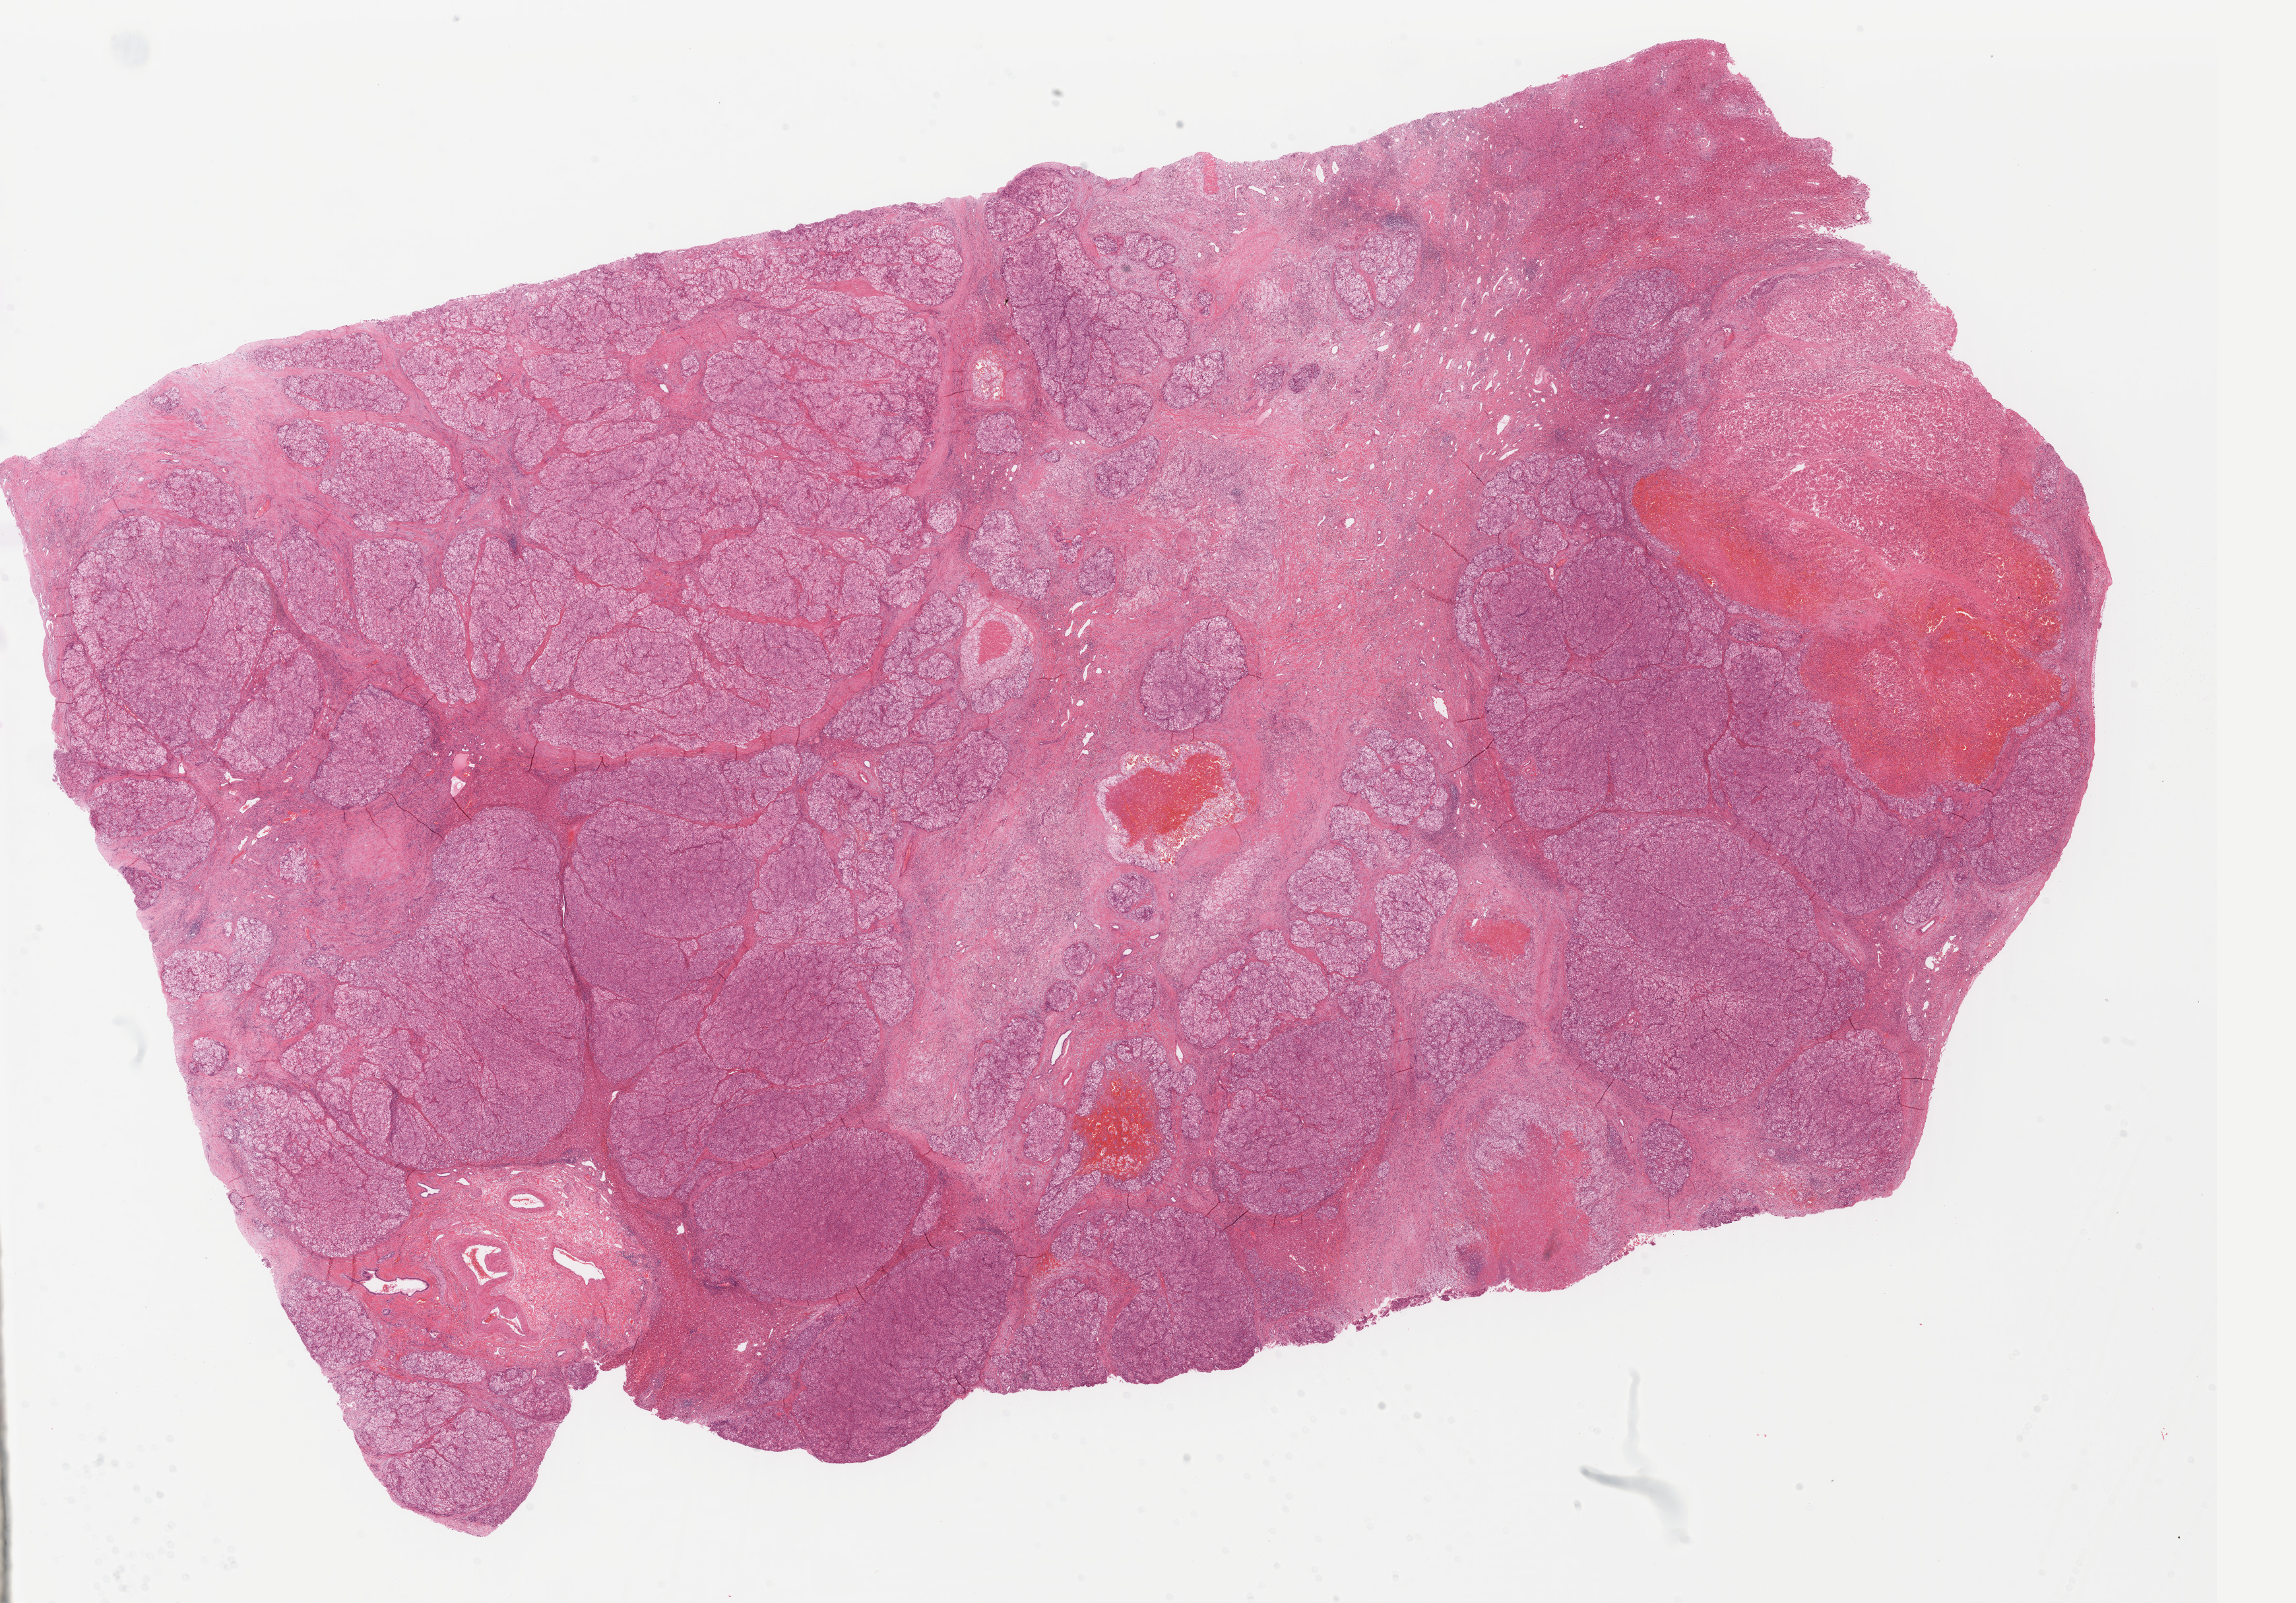
Whole-slide histology image, H&E-stained, a low-resolution overview of the entire scanned area, about 27.4 x 19.1 mm; FFPE section; liver, primary tumour sample. Patient: male, age at initial diagnosis 35 years. Histologic grade: G3 (poorly differentiated).
Pathologic diagnosis: Hepatocellular carcinoma, NOS. AJCC pathologic stage: IIIA.